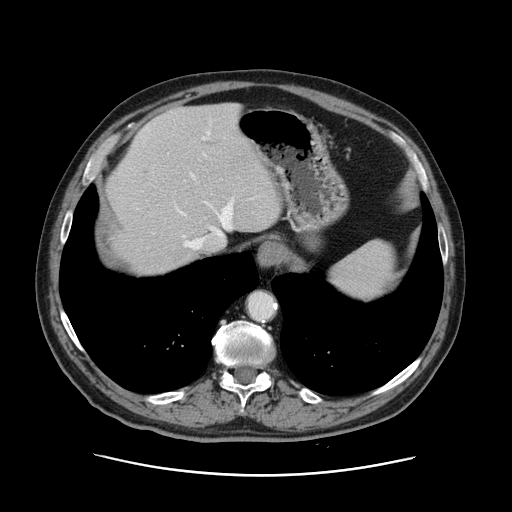
Contrast-enhanced abdominal CT, one axial slice; intravenous contrast given; soft-tissue window (W 400 / L 40 HU); 2.5 mm slice thickness; 512 × 512 image matrix, field of view 395 × 395 mm. Male patient, age 72 years. Case-level facts recorded for this patient, not image findings: diagnosis: colorectal cancer liver metastases, imaged before liver resection; multiple liver metastases: yes; largest metastasis: 5.4 cm; chemotherapy before resection: yes.
Annotated regions visible in this slice (expert manual segmentation):
- hepatic veins: bounding box (x1, y1, x2, y2) in pixels: (179, 132, 232, 250)
- liver: (107, 103, 280, 277)
- planned liver remnant (the part of the liver to remain after resection): (133, 103, 280, 277)
- portal vein (with intrahepatic branches): (189, 130, 231, 249)